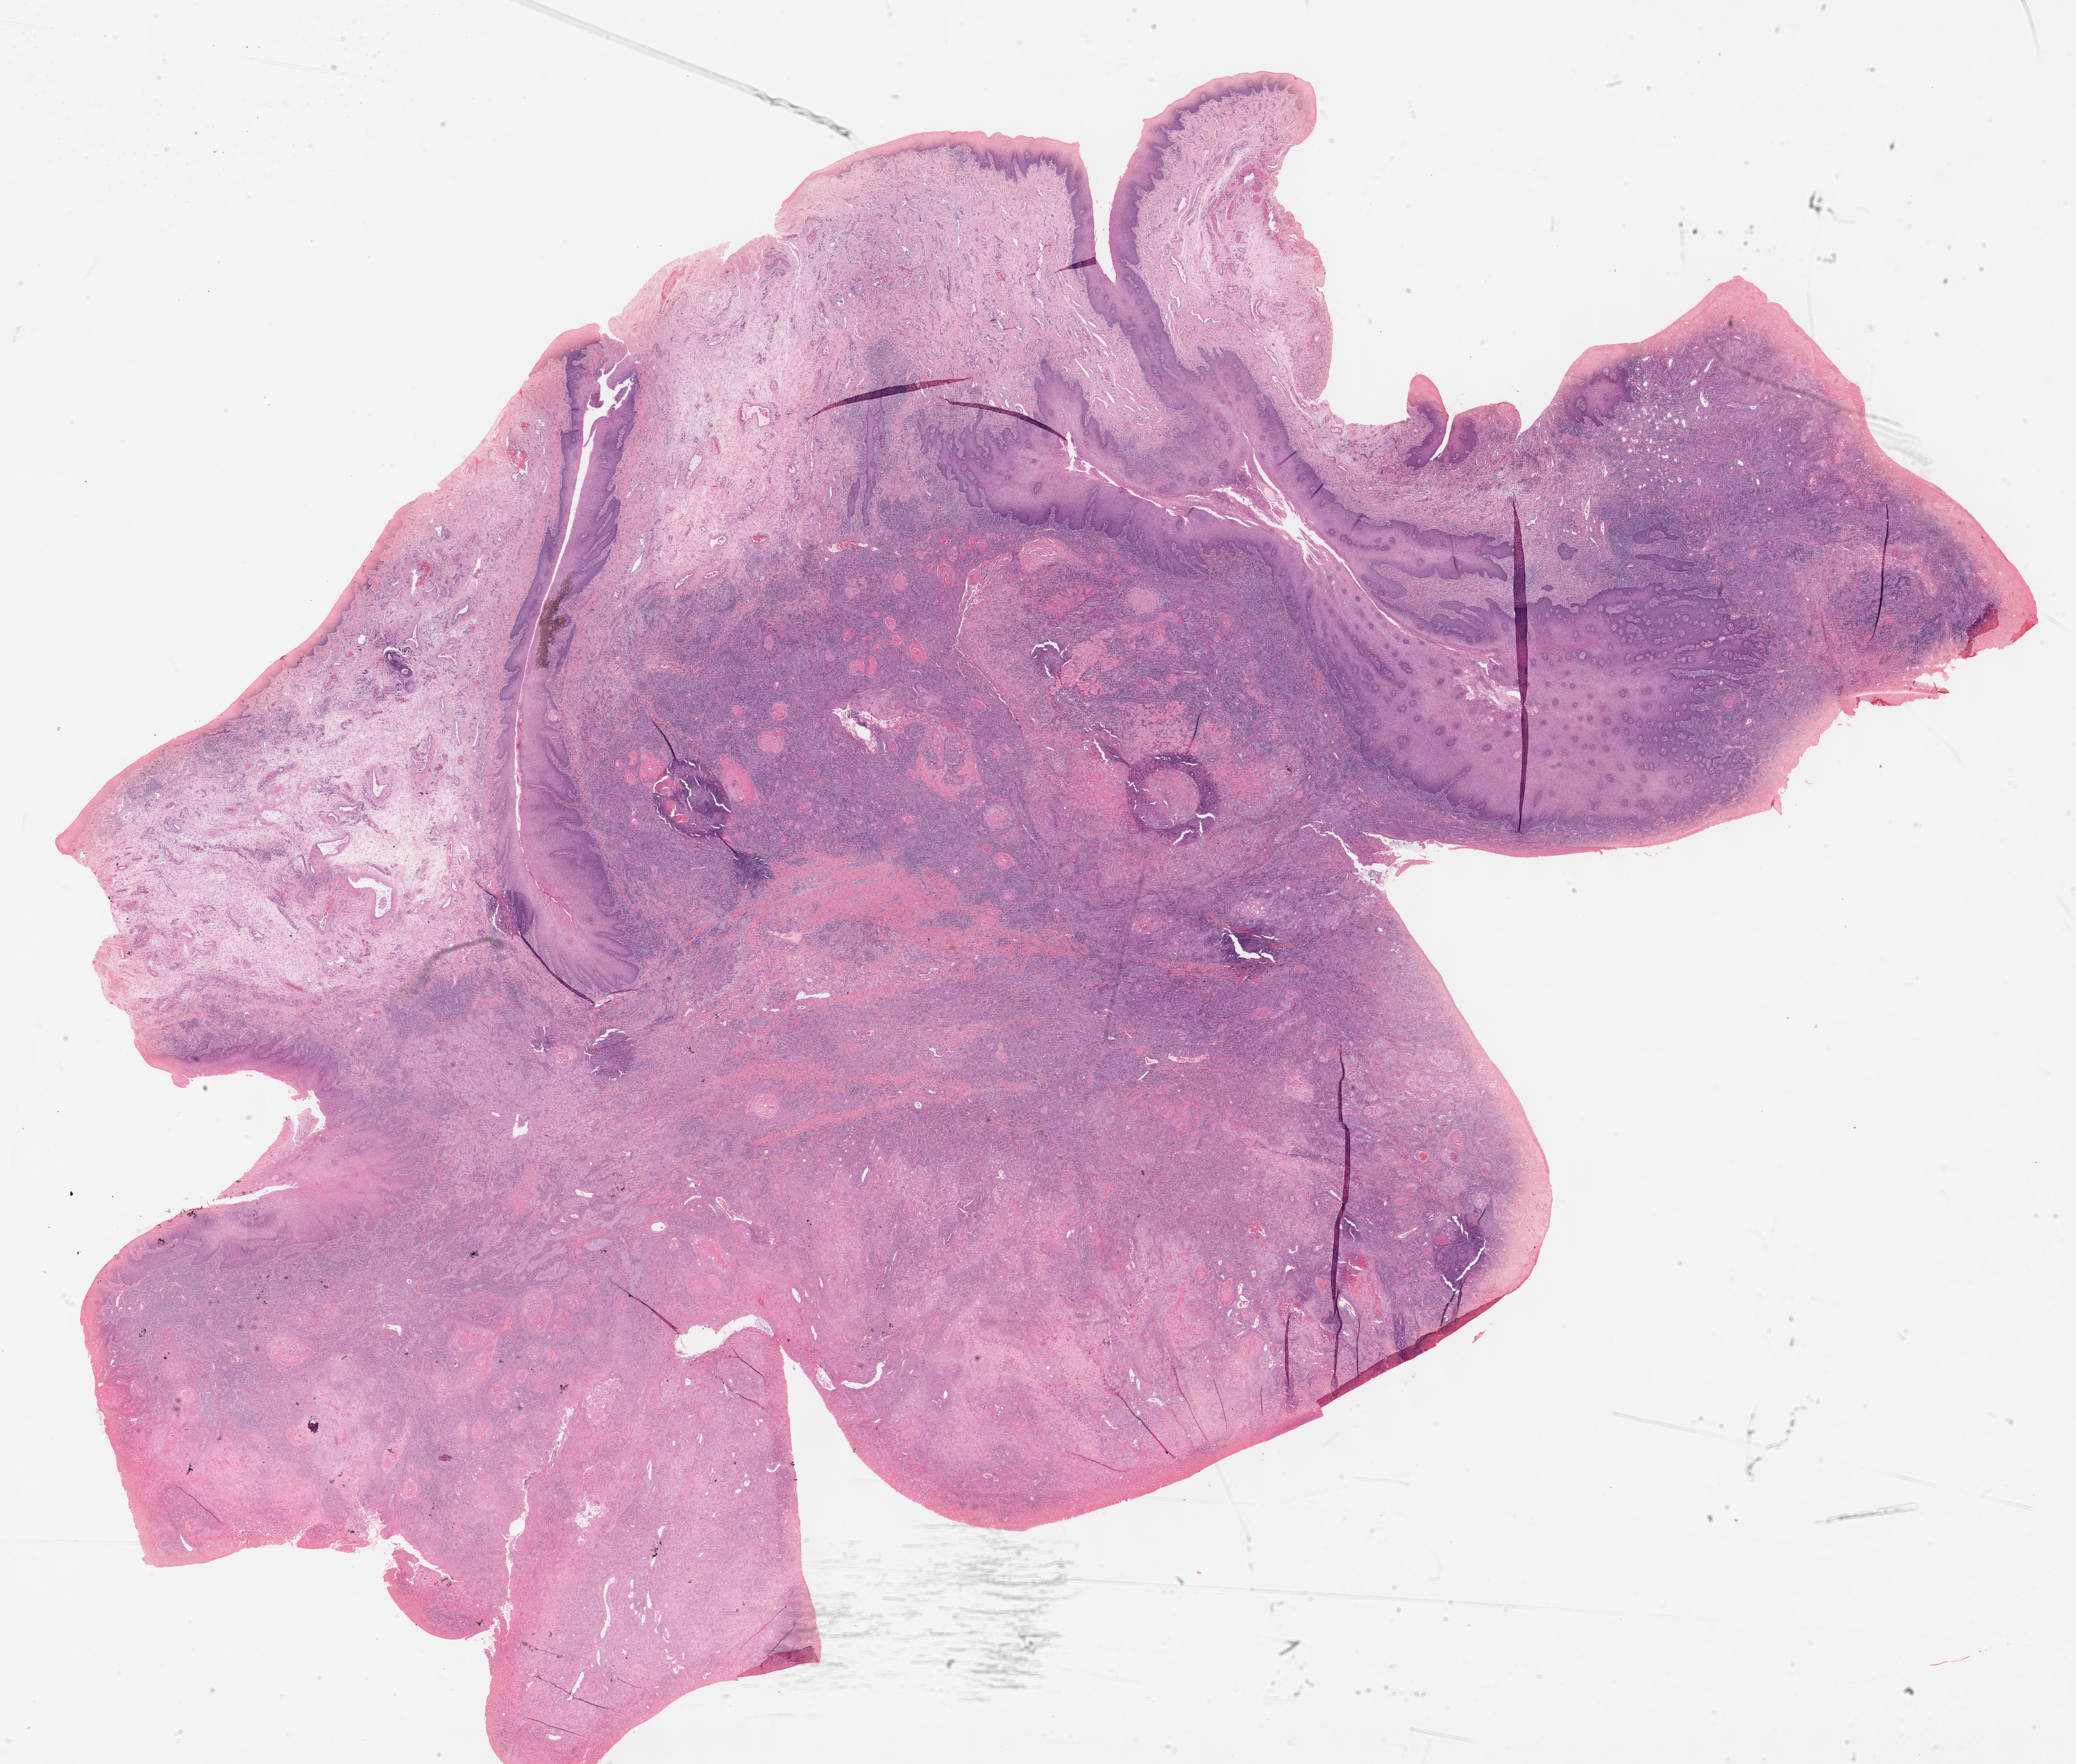
Hematoxylin and eosin (H&E) stained whole-slide image, shown as a low-resolution overview of the whole scanned area (about 26.2 x 22.2 mm). FFPE section. Head and neck, primary tumour sample. Male, age 74 years at initial diagnosis. Histologic grade: G2 (moderately differentiated).
AJCC pathologic stage: IVA (7th edition). TNM: T4a N2c. Diagnosis: Squamous cell carcinoma, NOS.